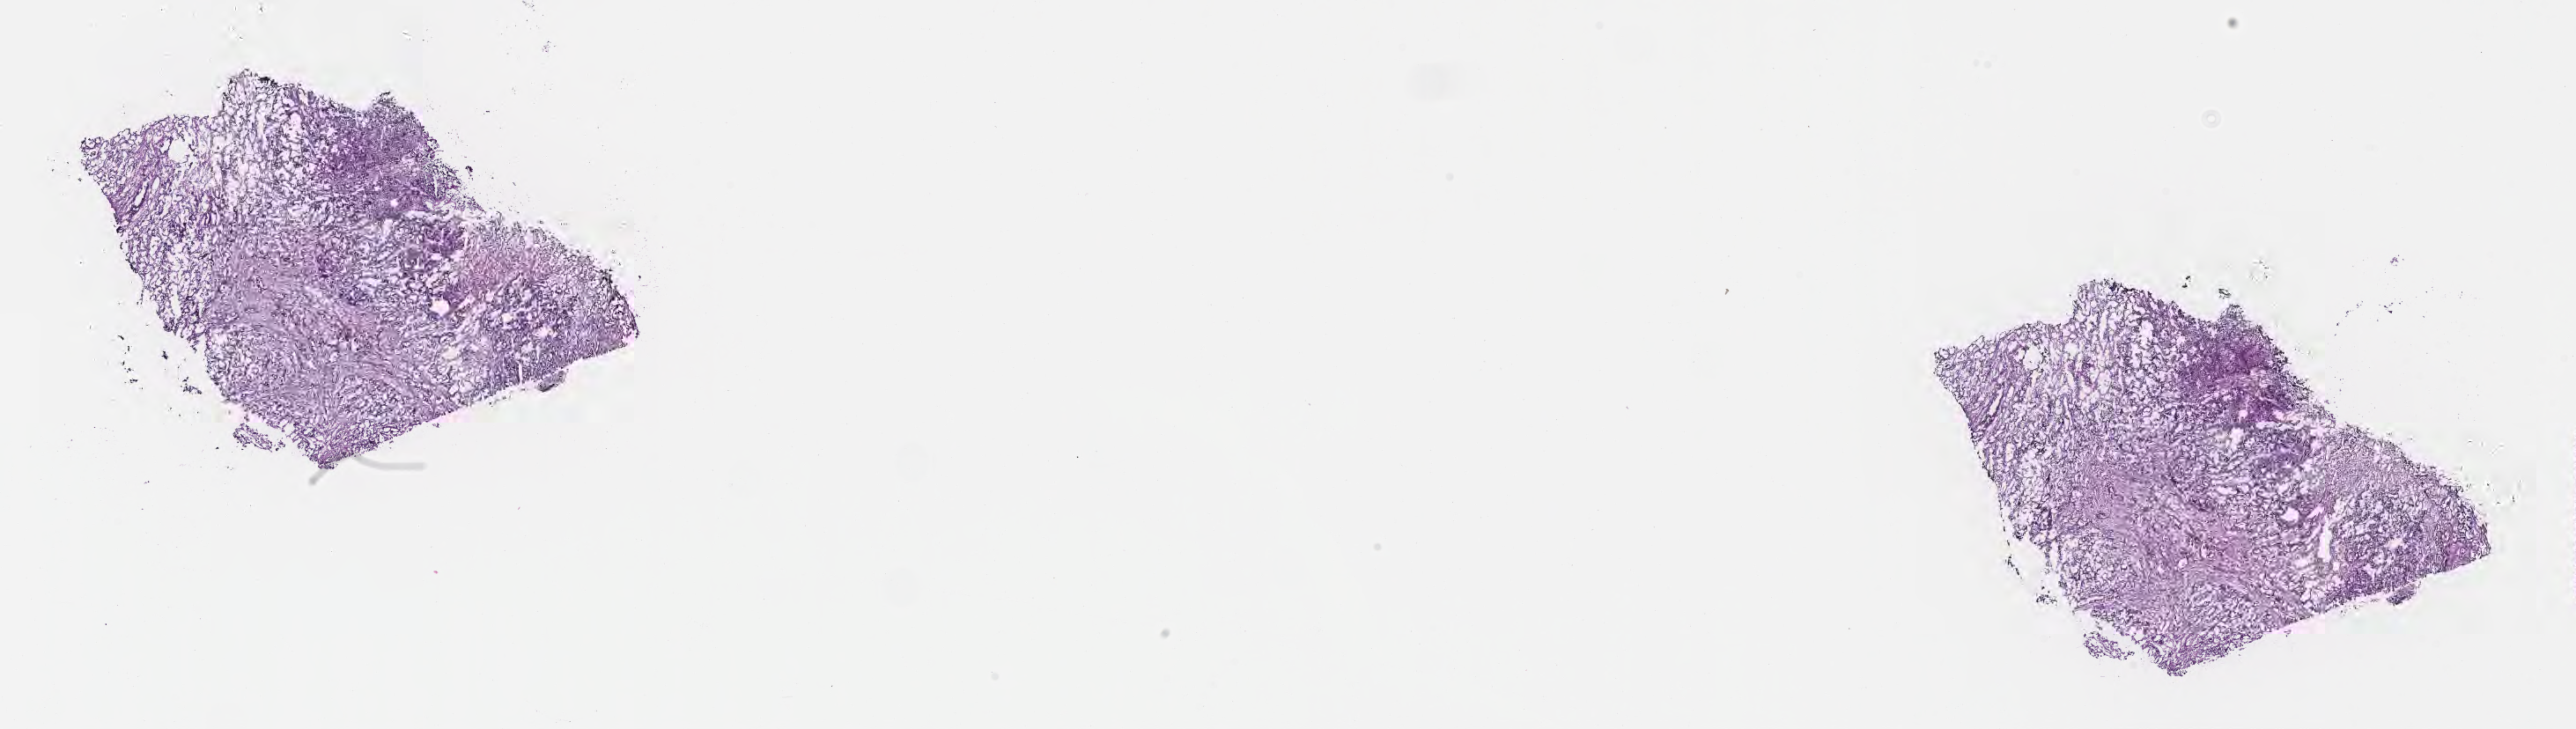
Digitized haematoxylin and eosin-stained section — low-resolution overview of the scanned area, about 23.6 x 6.7 mm. Frozen section (tissue freezing medium). Metastatic tumor tissue, resected from liver. Female, age 78 years at initial diagnosis. Pathologist review of this section (percent, as recorded): tumor cells 40%, tumor nuclei 40%, stromal cells 60%, necrosis 0%, normal cells 0%. Infiltration values recorded for this section: lymphocyte infiltration 0%, monocyte infiltration 0%, neutrophil infiltration 0%.
Patient diagnosis (primary): Adenocarcinoma, NOS.